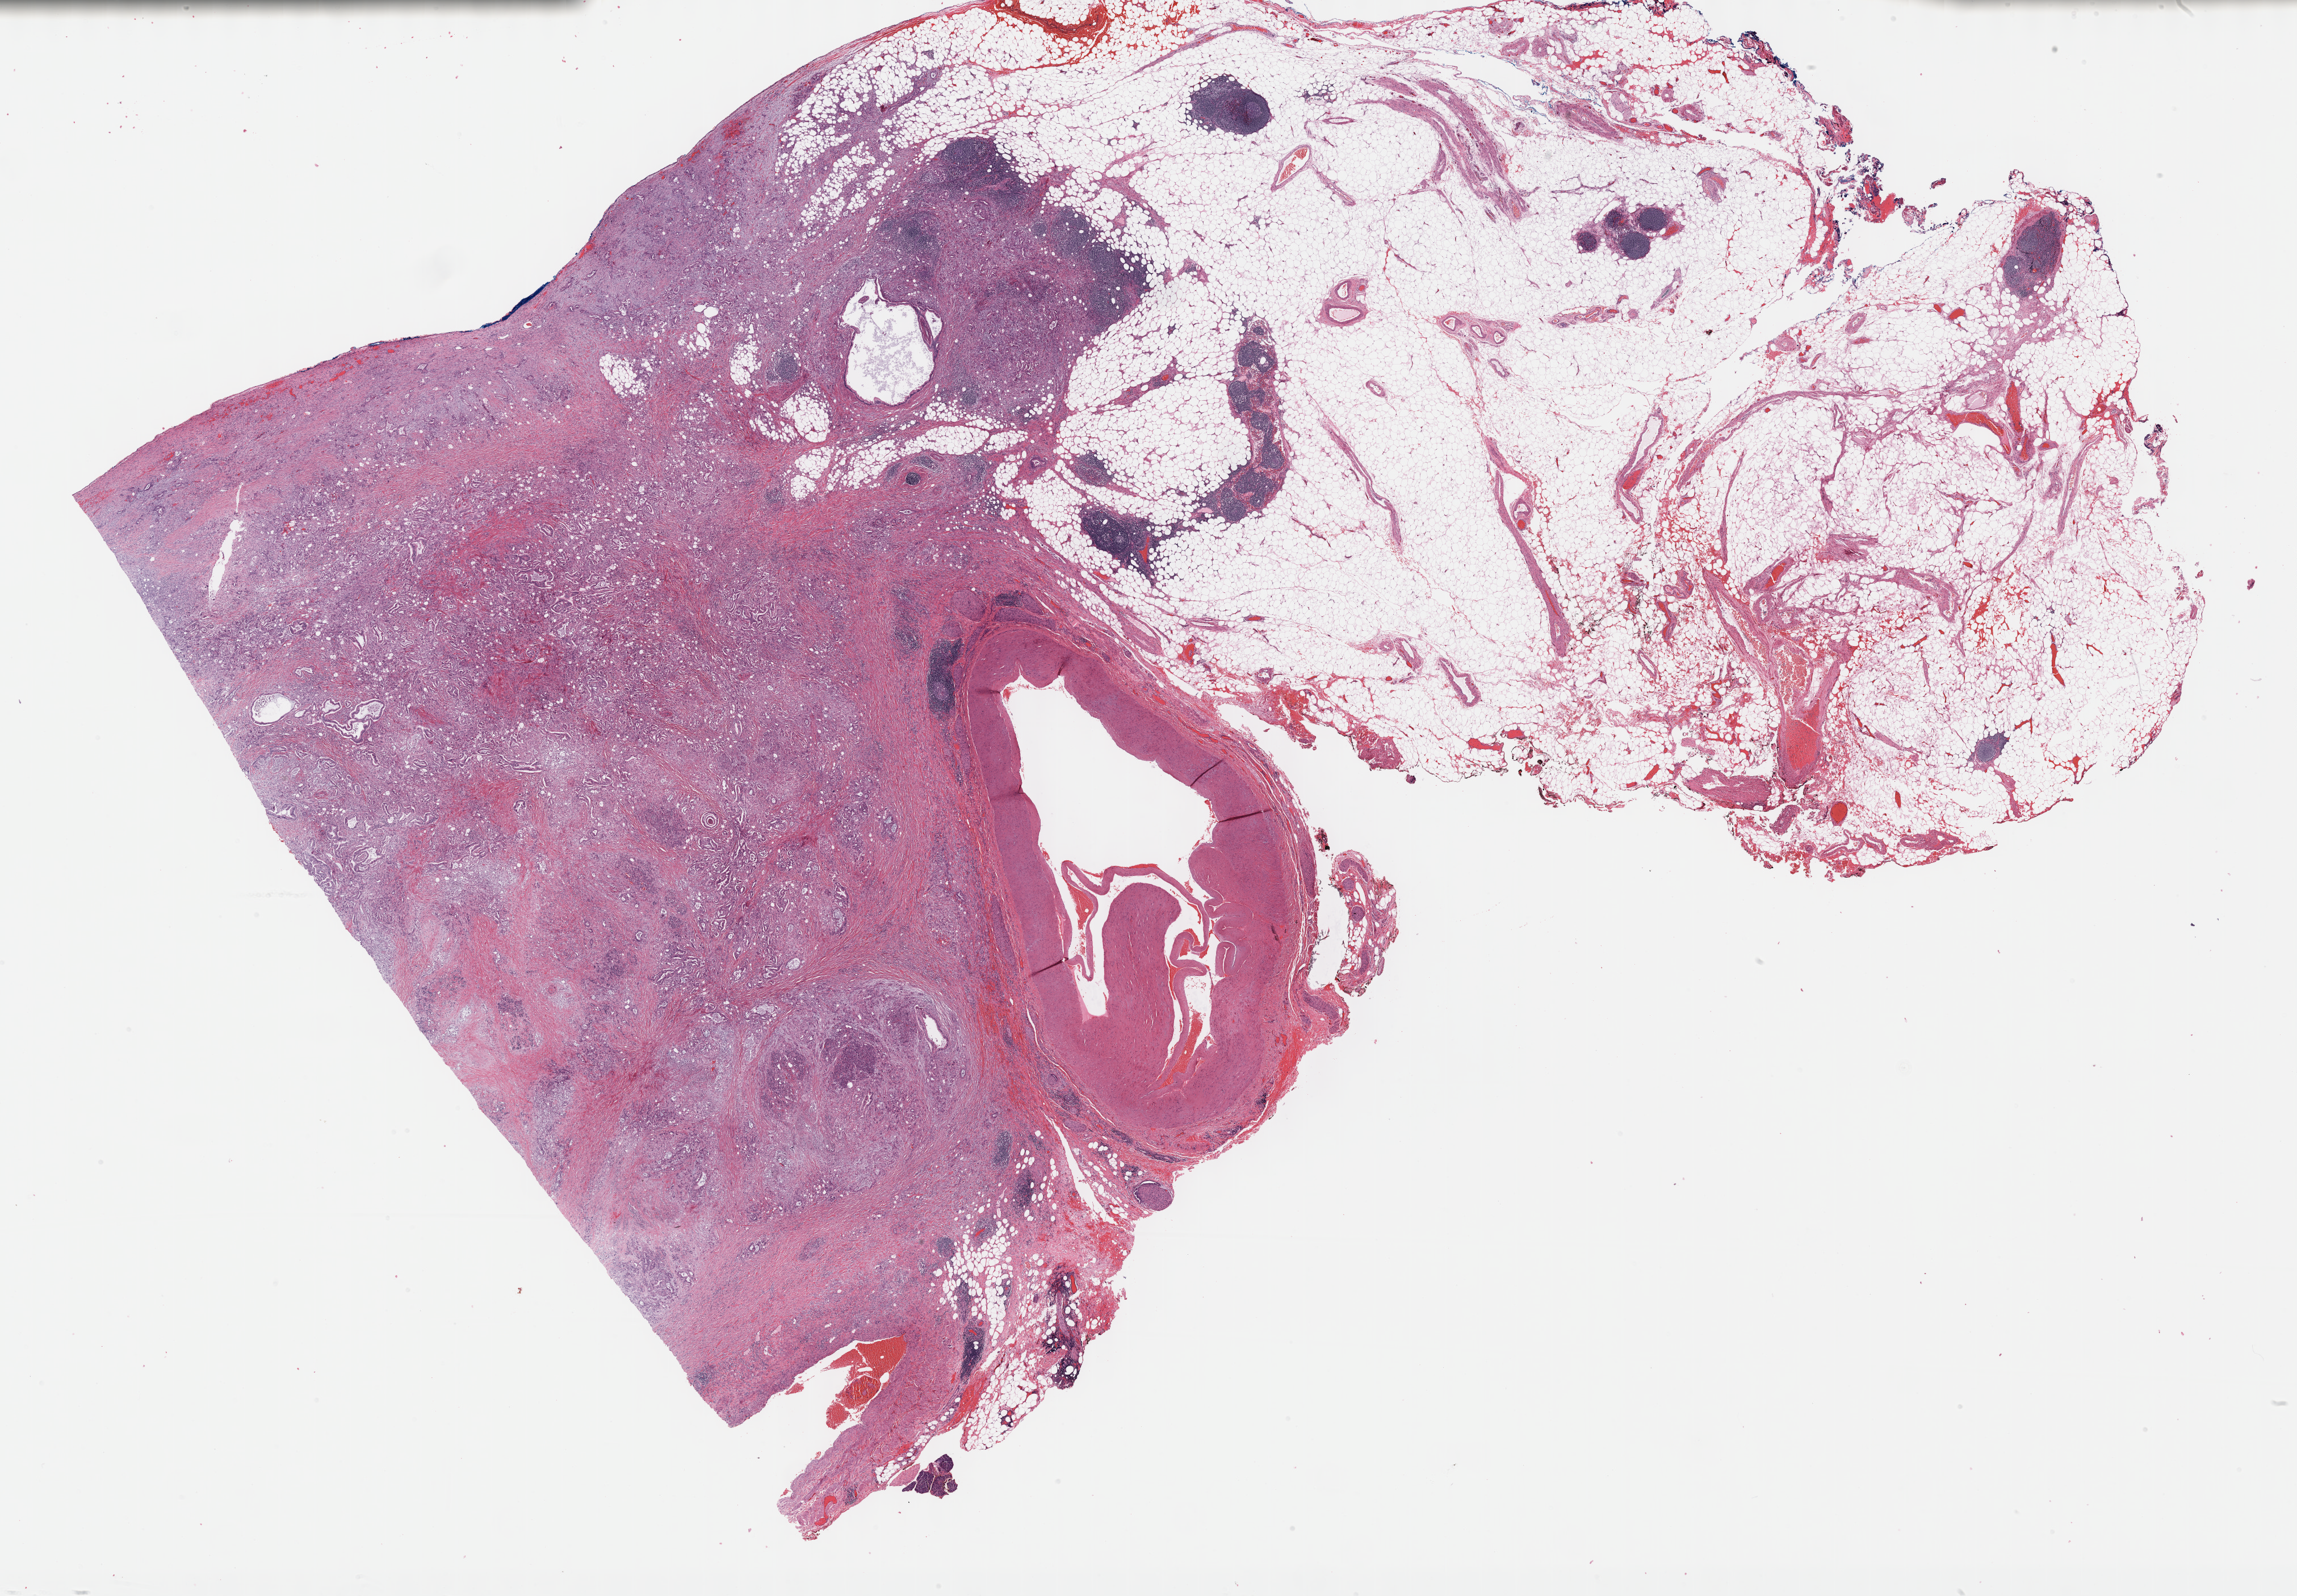
H&E-stained whole-slide image — whole scanned area (about 32.7 x 22.7 mm) shown as a low-resolution overview, formalin-fixed paraffin-embedded (FFPE) diagnostic section, pancreas, primary tumour sample. Patient: female, age at initial diagnosis 64 years. Histologic grade: G3 (poorly differentiated).
Diagnosis: Infiltrating duct carcinoma, NOS (head of pancreas). AJCC pathologic stage: IIB (7th edition). Lymph nodes positive (case pathology): 5 of 7 examined.